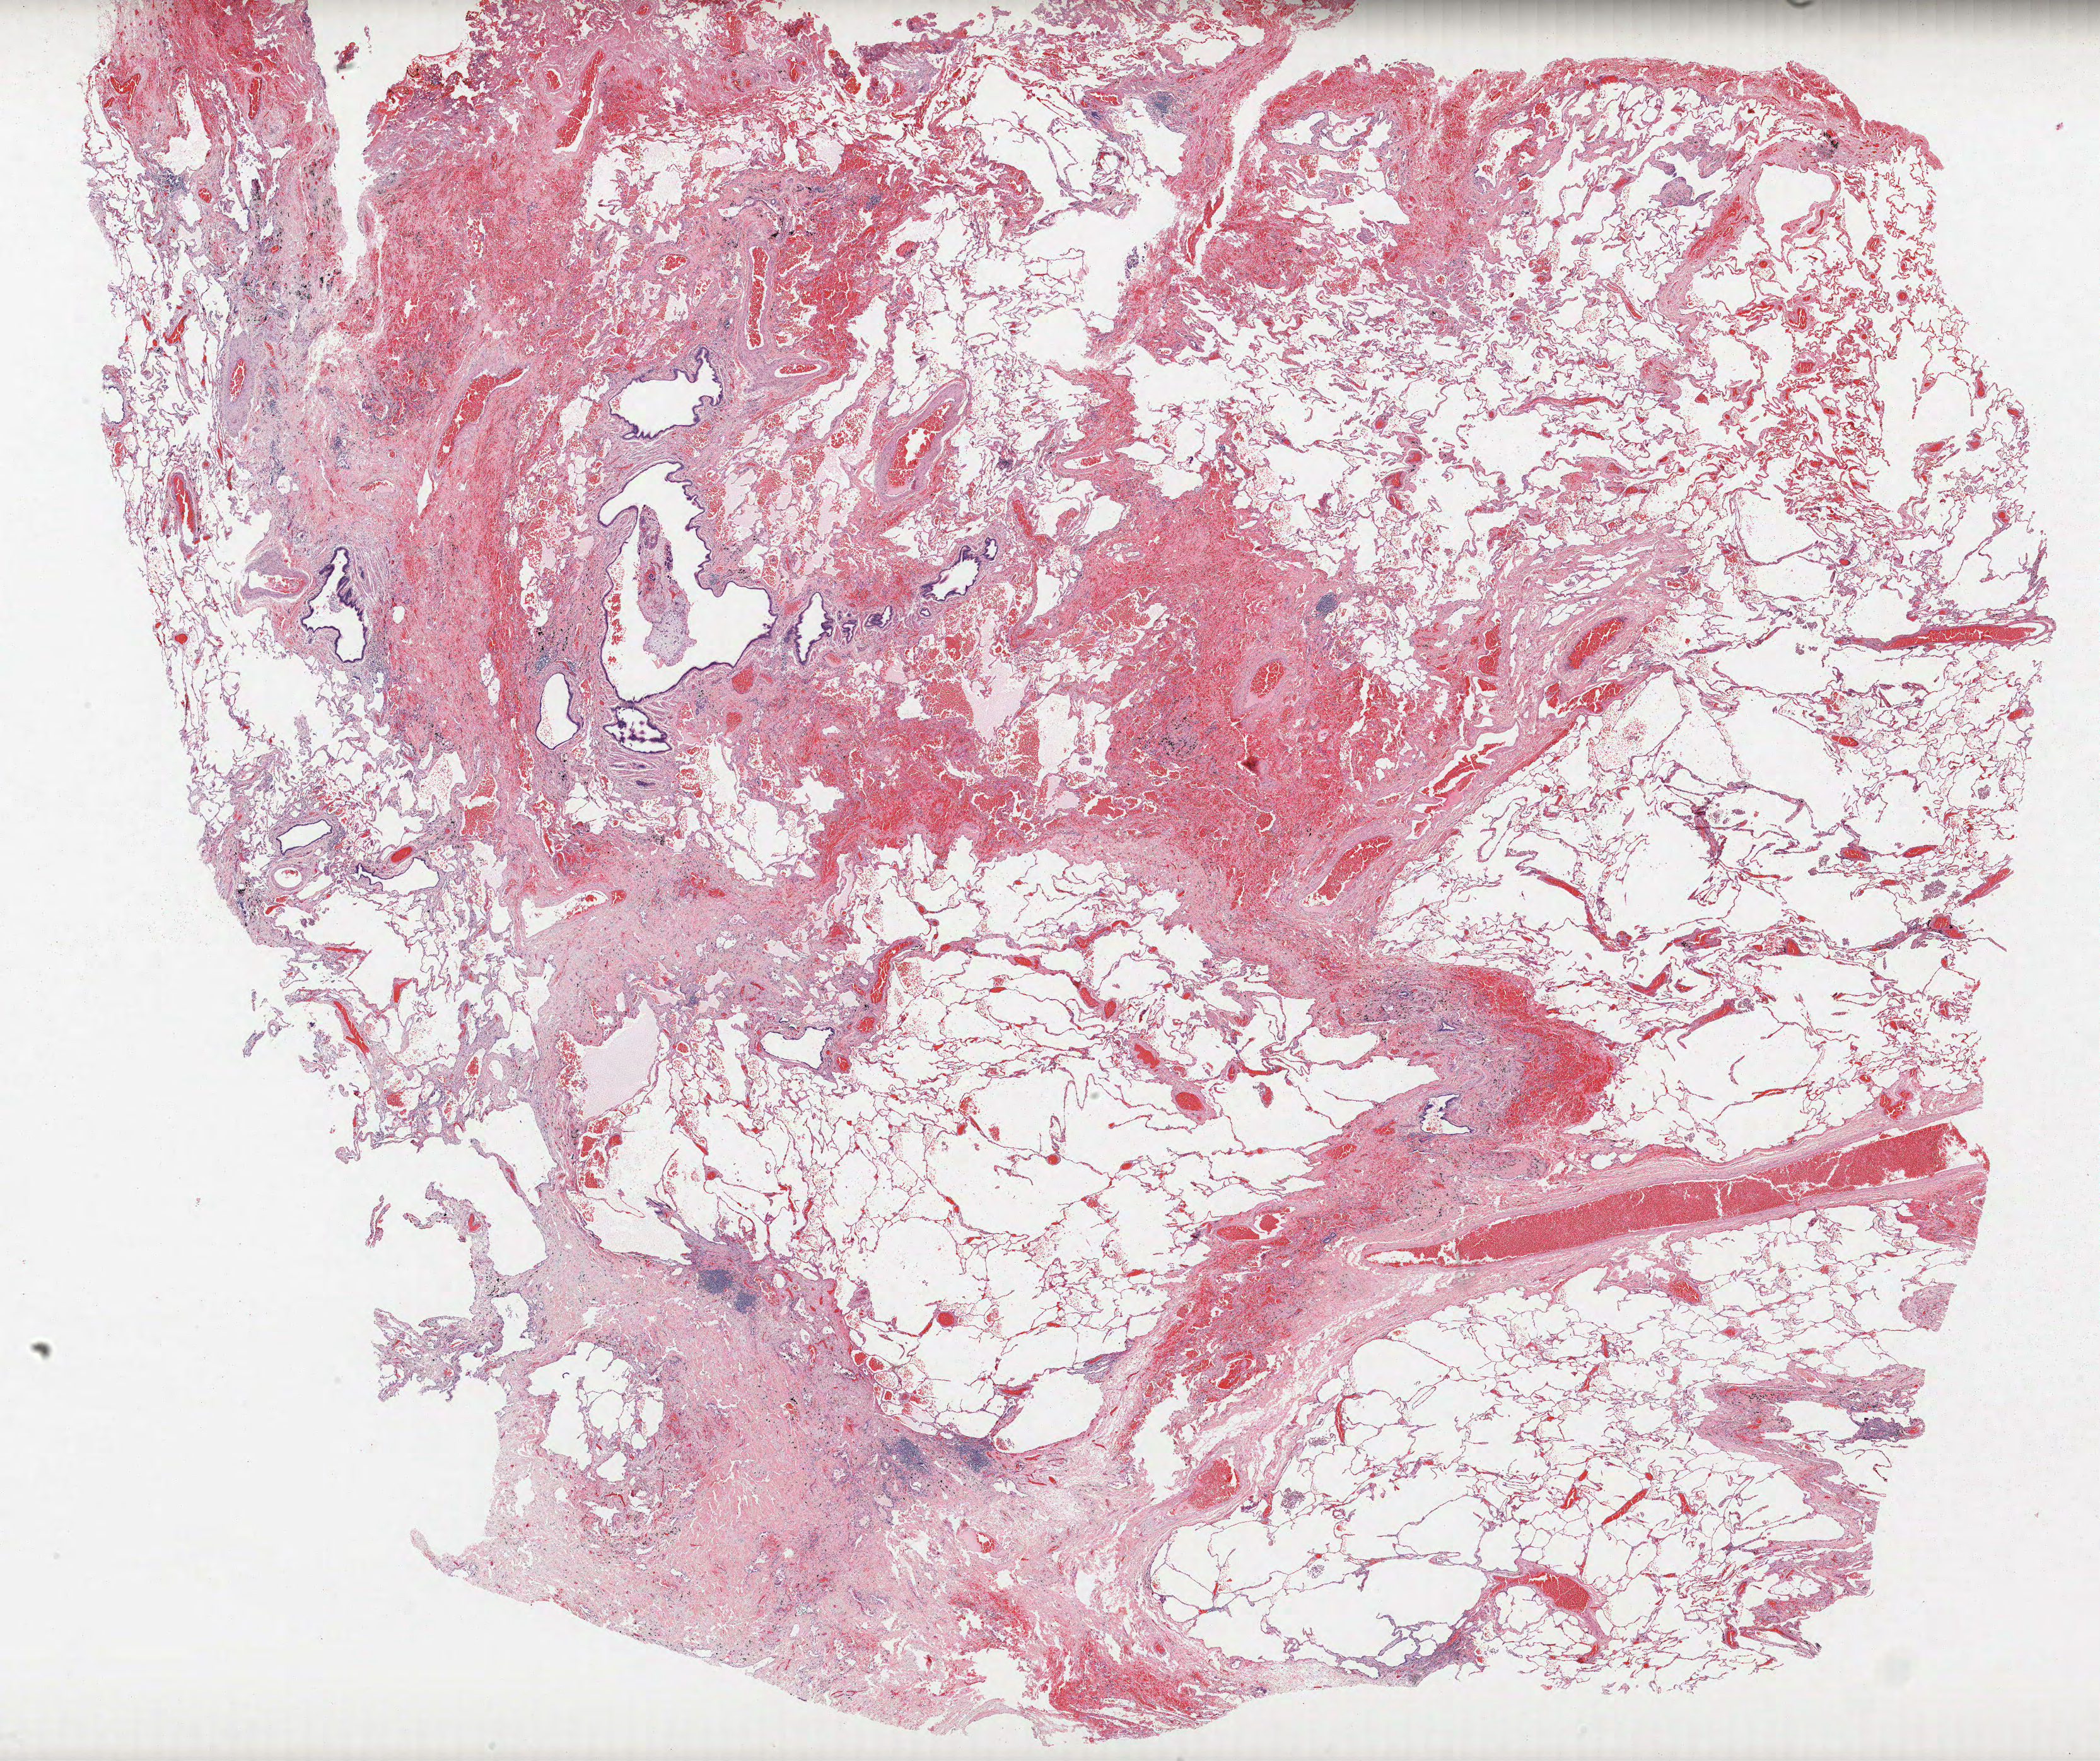
Whole-slide histology image, Hematoxylin and eosin (H&E) stained, whole scanned area (about 26.6 x 22.3 mm, acquisition: 40x scan) shown as a low-resolution overview. Formalin-fixed paraffin-embedded (FFPE) section. Lung tissue. Male patient, aged 65 at enrolment. Current smoker at enrolment. Grade: moderately differentiated (G2).
Stage (AJCC 6th edition): IA. Participant's lung-cancer diagnosis: Squamous cell carcinoma, NOS (ICD-O-3 8070/3). Primary tumour location (clinical record): left upper lobe. Tumour size (pathology): 25 mm.